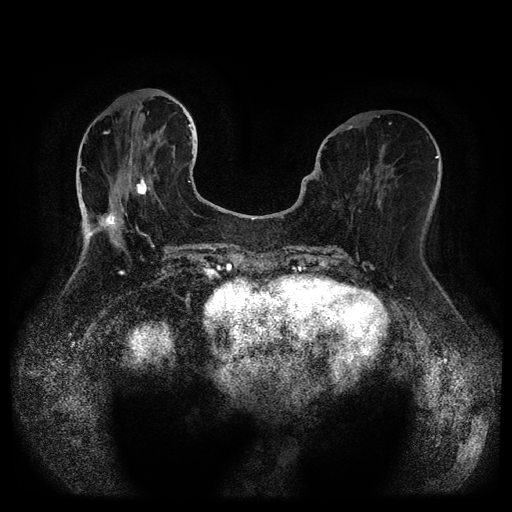
Breast MRI (dynamic contrast-enhanced, multi-phase), one axial slice. Position 38 of 116 along the scan axis. Dynamic contrast-enhanced series, time point 2 of 5 at this slice position (early post-contrast). 1.5 T. TE 2.6 ms, TR 5.3 ms. 2 mm slice thickness. 512 × 512 image matrix, field of view 350 × 350 mm. Patient: female, 75 years.
Structures marked on this image (semi-automatic segmentation, software-assisted and operator-edited):
- breast lesion (labelled benign in the annotation): bounding box <131,174,150,201> (left, top, right, bottom; pixels)
- breast lesion (labelled benign in the annotation): <97,212,120,229>